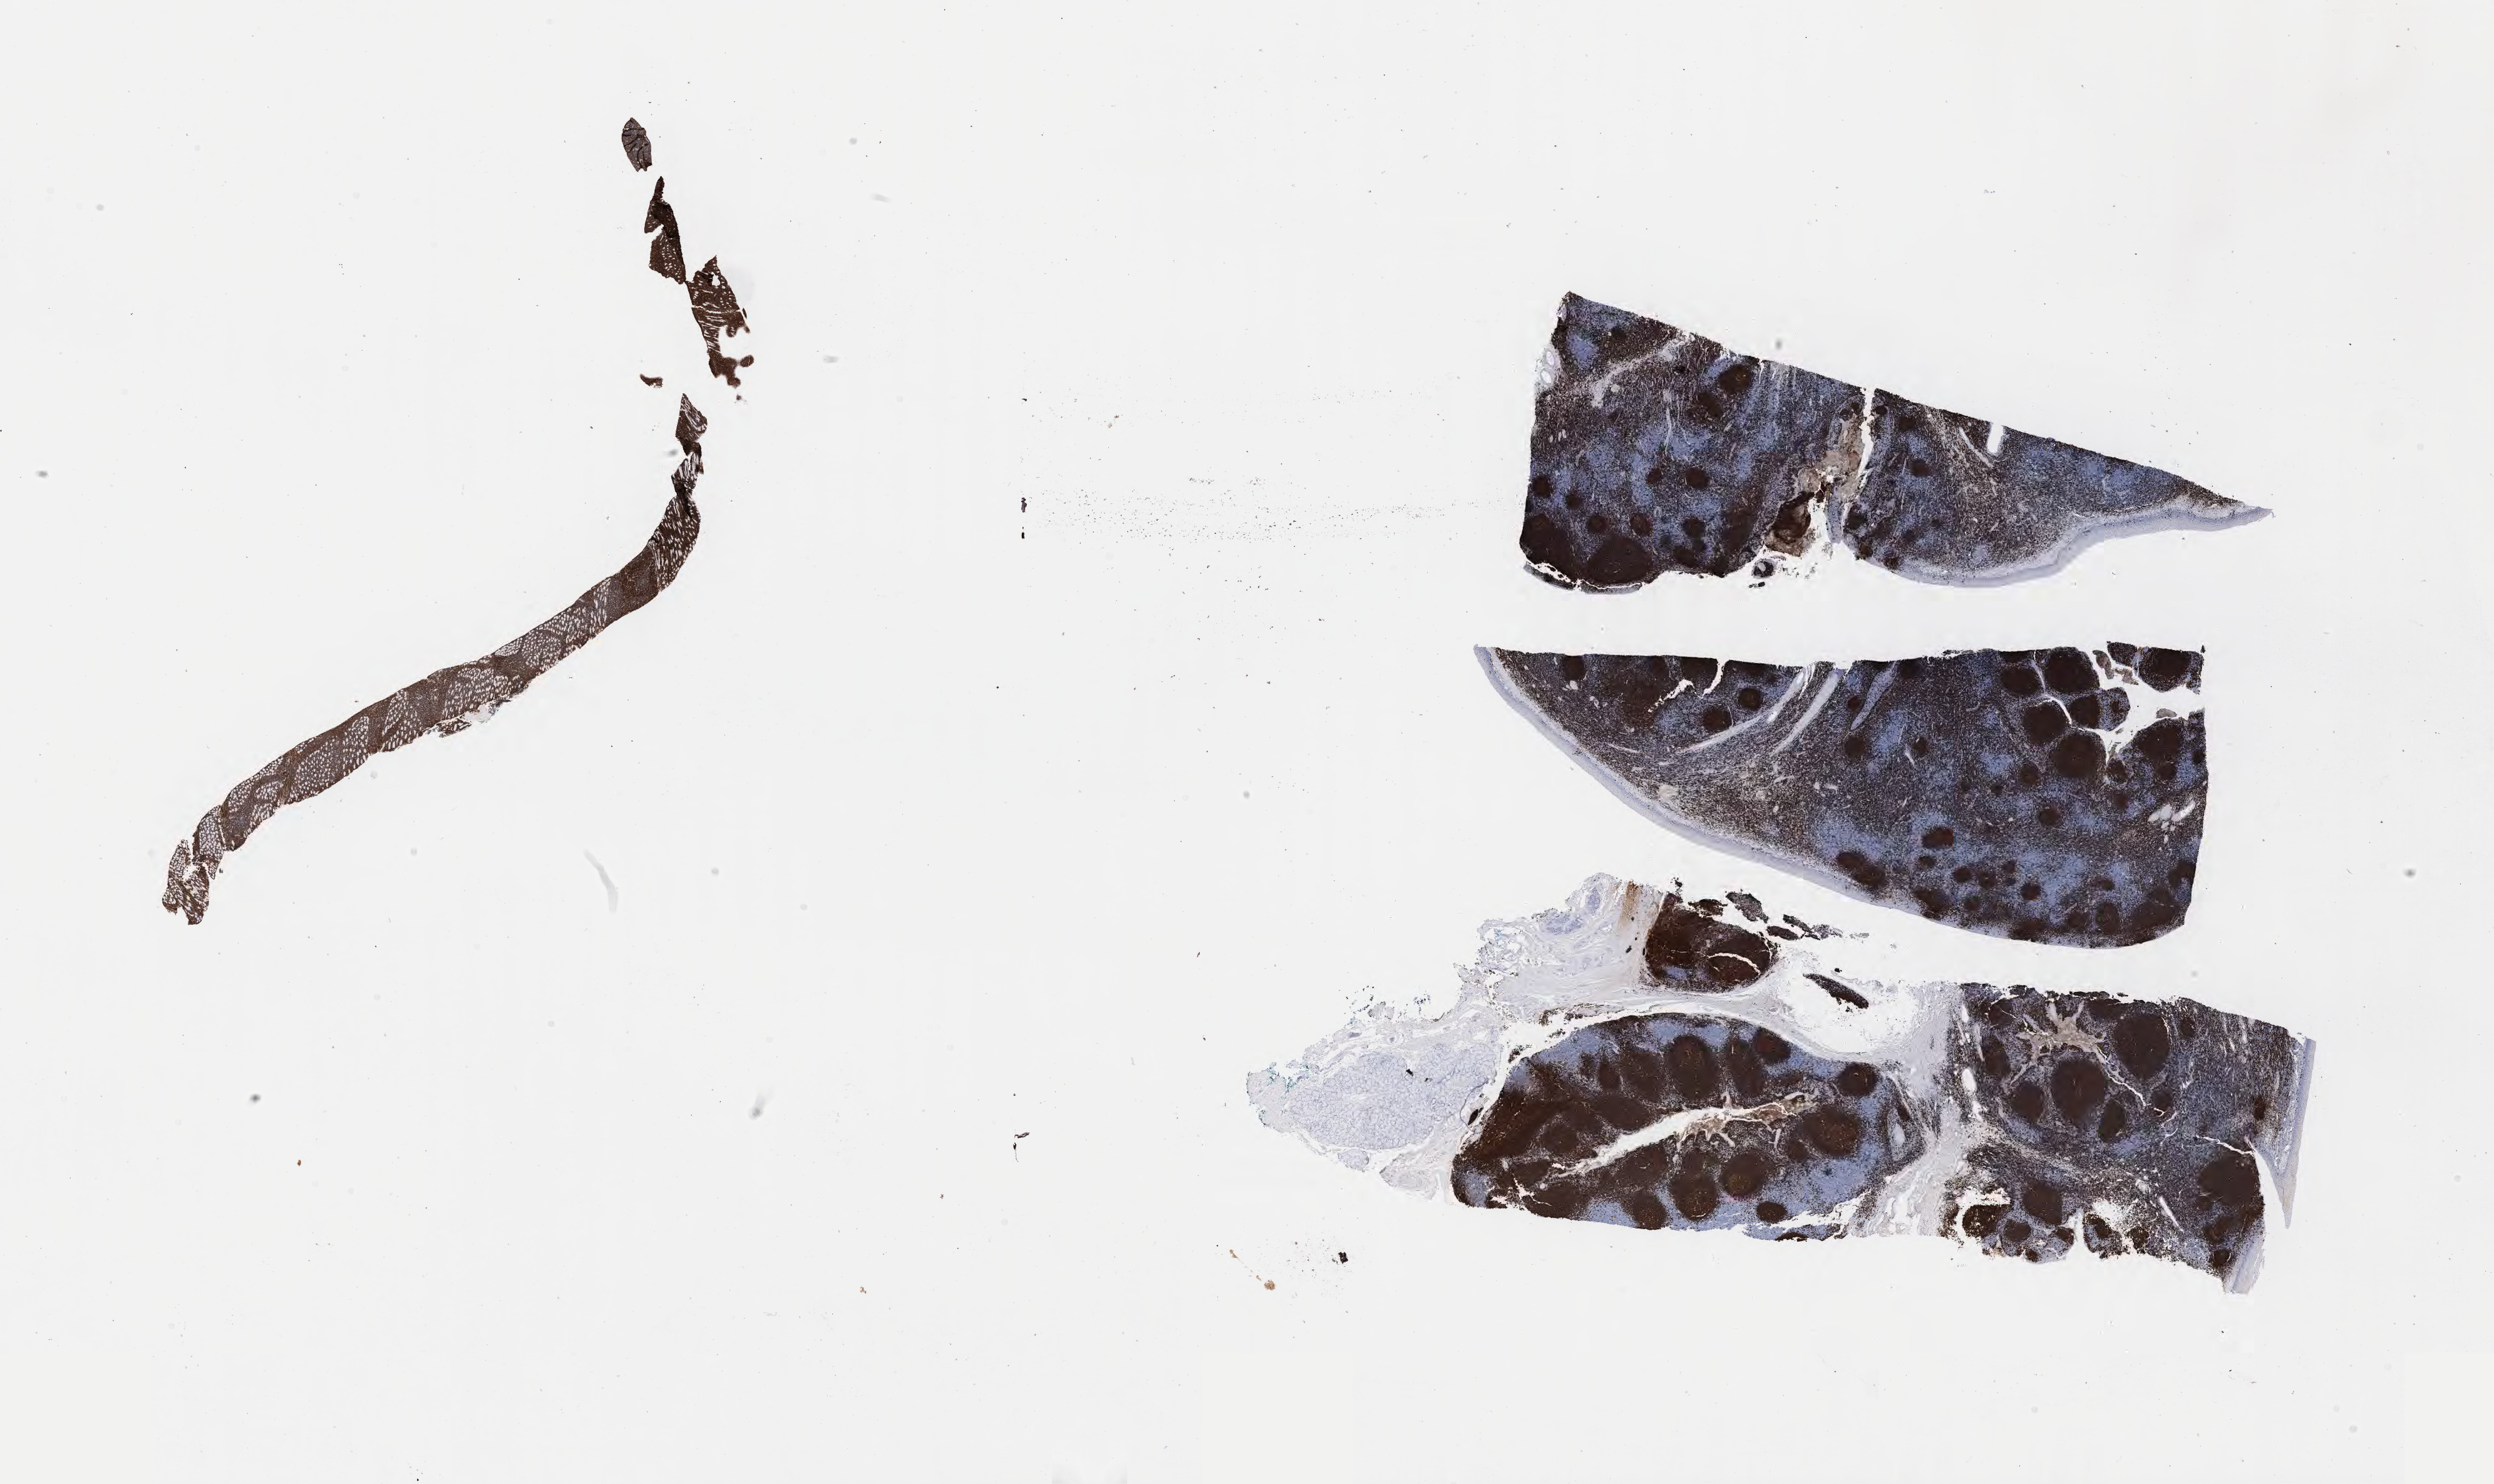
Immunohistochemistry (IHC) whole-slide image stained for CD20 — low-resolution overview of the scanned area, about 32.2 x 19.2 mm; specimen: tumor tissue. Male, age 4 years at initial diagnosis.
Histologic diagnosis: Burkitt lymphoma, NOS.